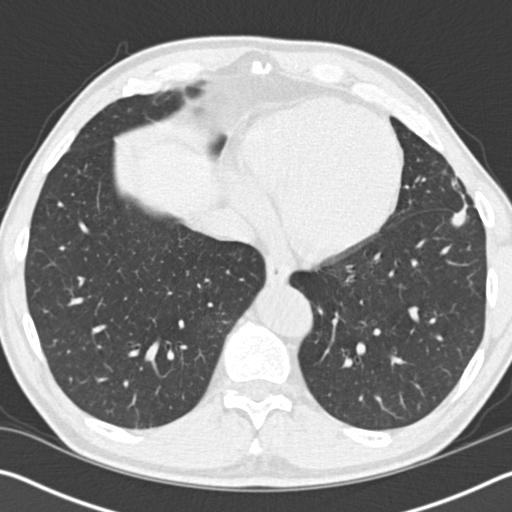
Low-dose screening chest CT, one axial slice. Position 43 of 162 along the scan axis. Reconstruction kernel B30f. 120 kVp. Lung window (W 1500 / L -600 HU). 2 mm slice thickness. 512 × 512 image matrix.
Annotated regions visible in this slice (manually delineated by an expert):
- lesion 1 (tumor, upper lobe of left lung): box from (x=451, y=179) to (x=468, y=227) px